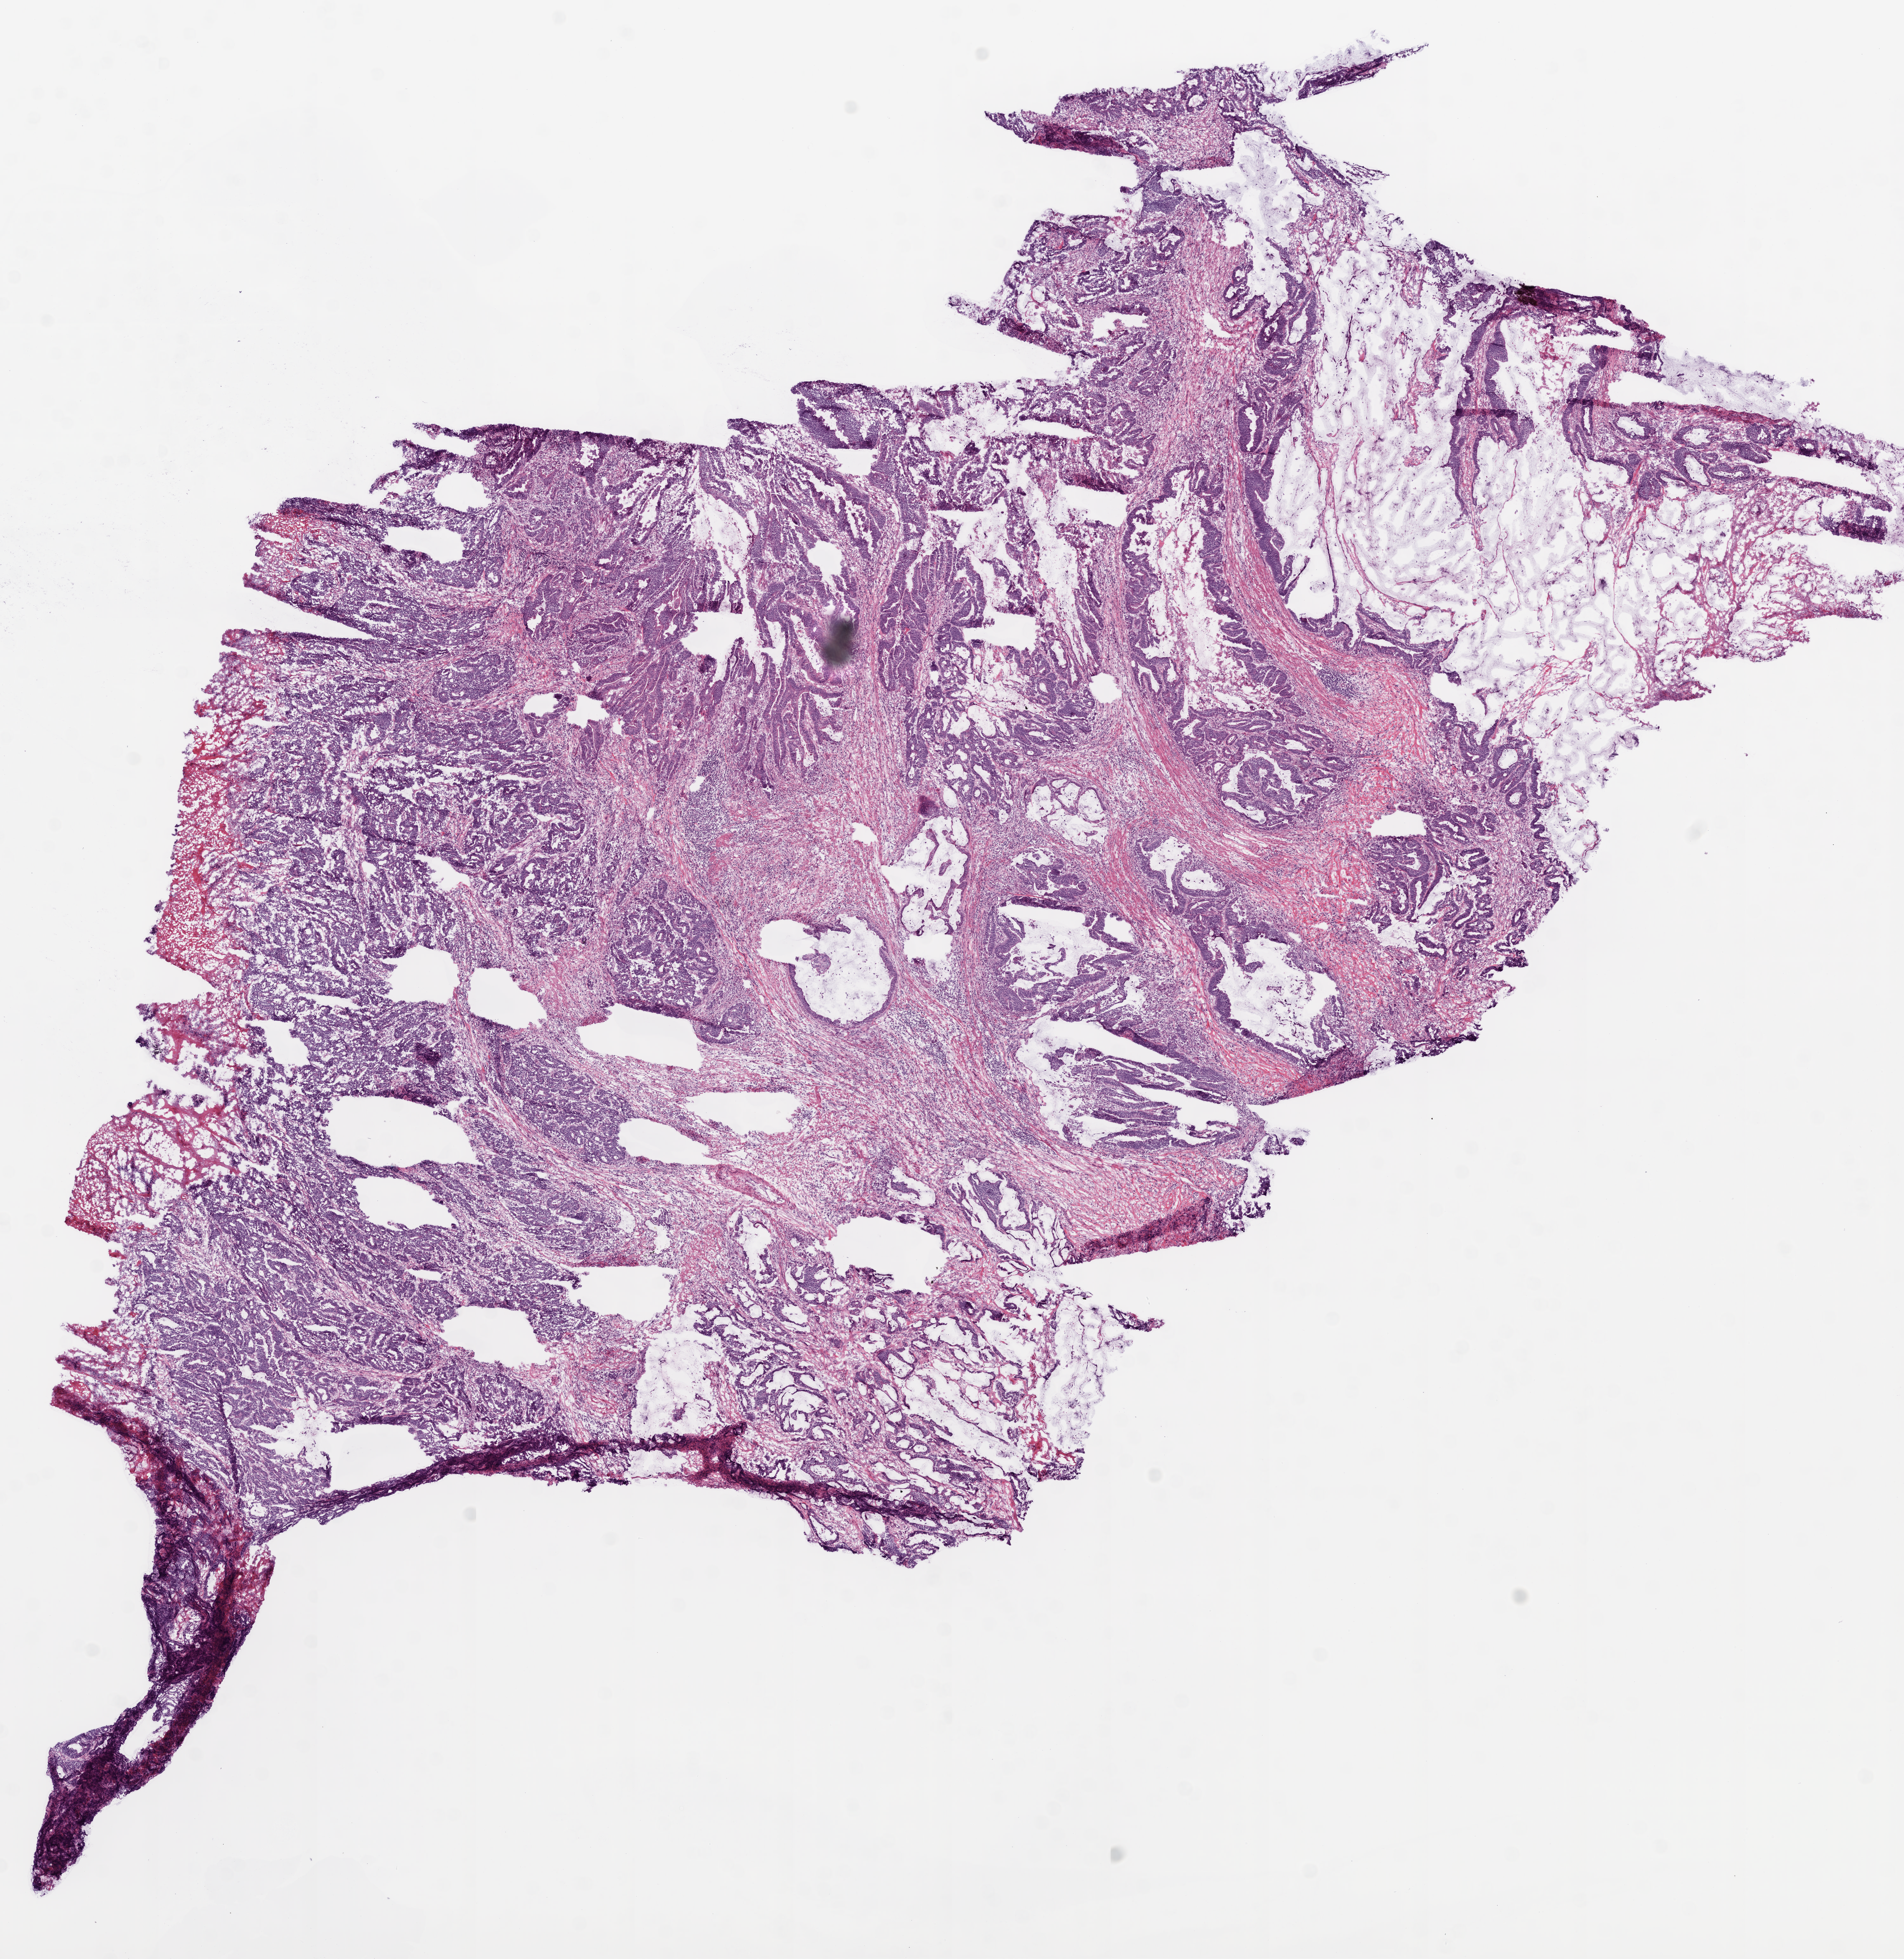
Whole-slide histology image, H&E-stained, a low-resolution overview of the entire scanned area, about 12.0 x 12.4 mm (acquisition: 20x scan), frozen section from the bottom of the tissue portion, colon, primary tumour sample. Female, age 60 years at initial diagnosis. Composition of this section per pathologist review: tumour cells 80%, tumour nuclei 70%, normal cells 0%, stromal cells 15%, necrosis 5%.
* lymph nodes positive (case pathology): 0 of 22 examined
* AJCC pathologic stage: IIB
* TNM: T4 N0 M0
* histologic diagnosis: Mucinous adenocarcinoma